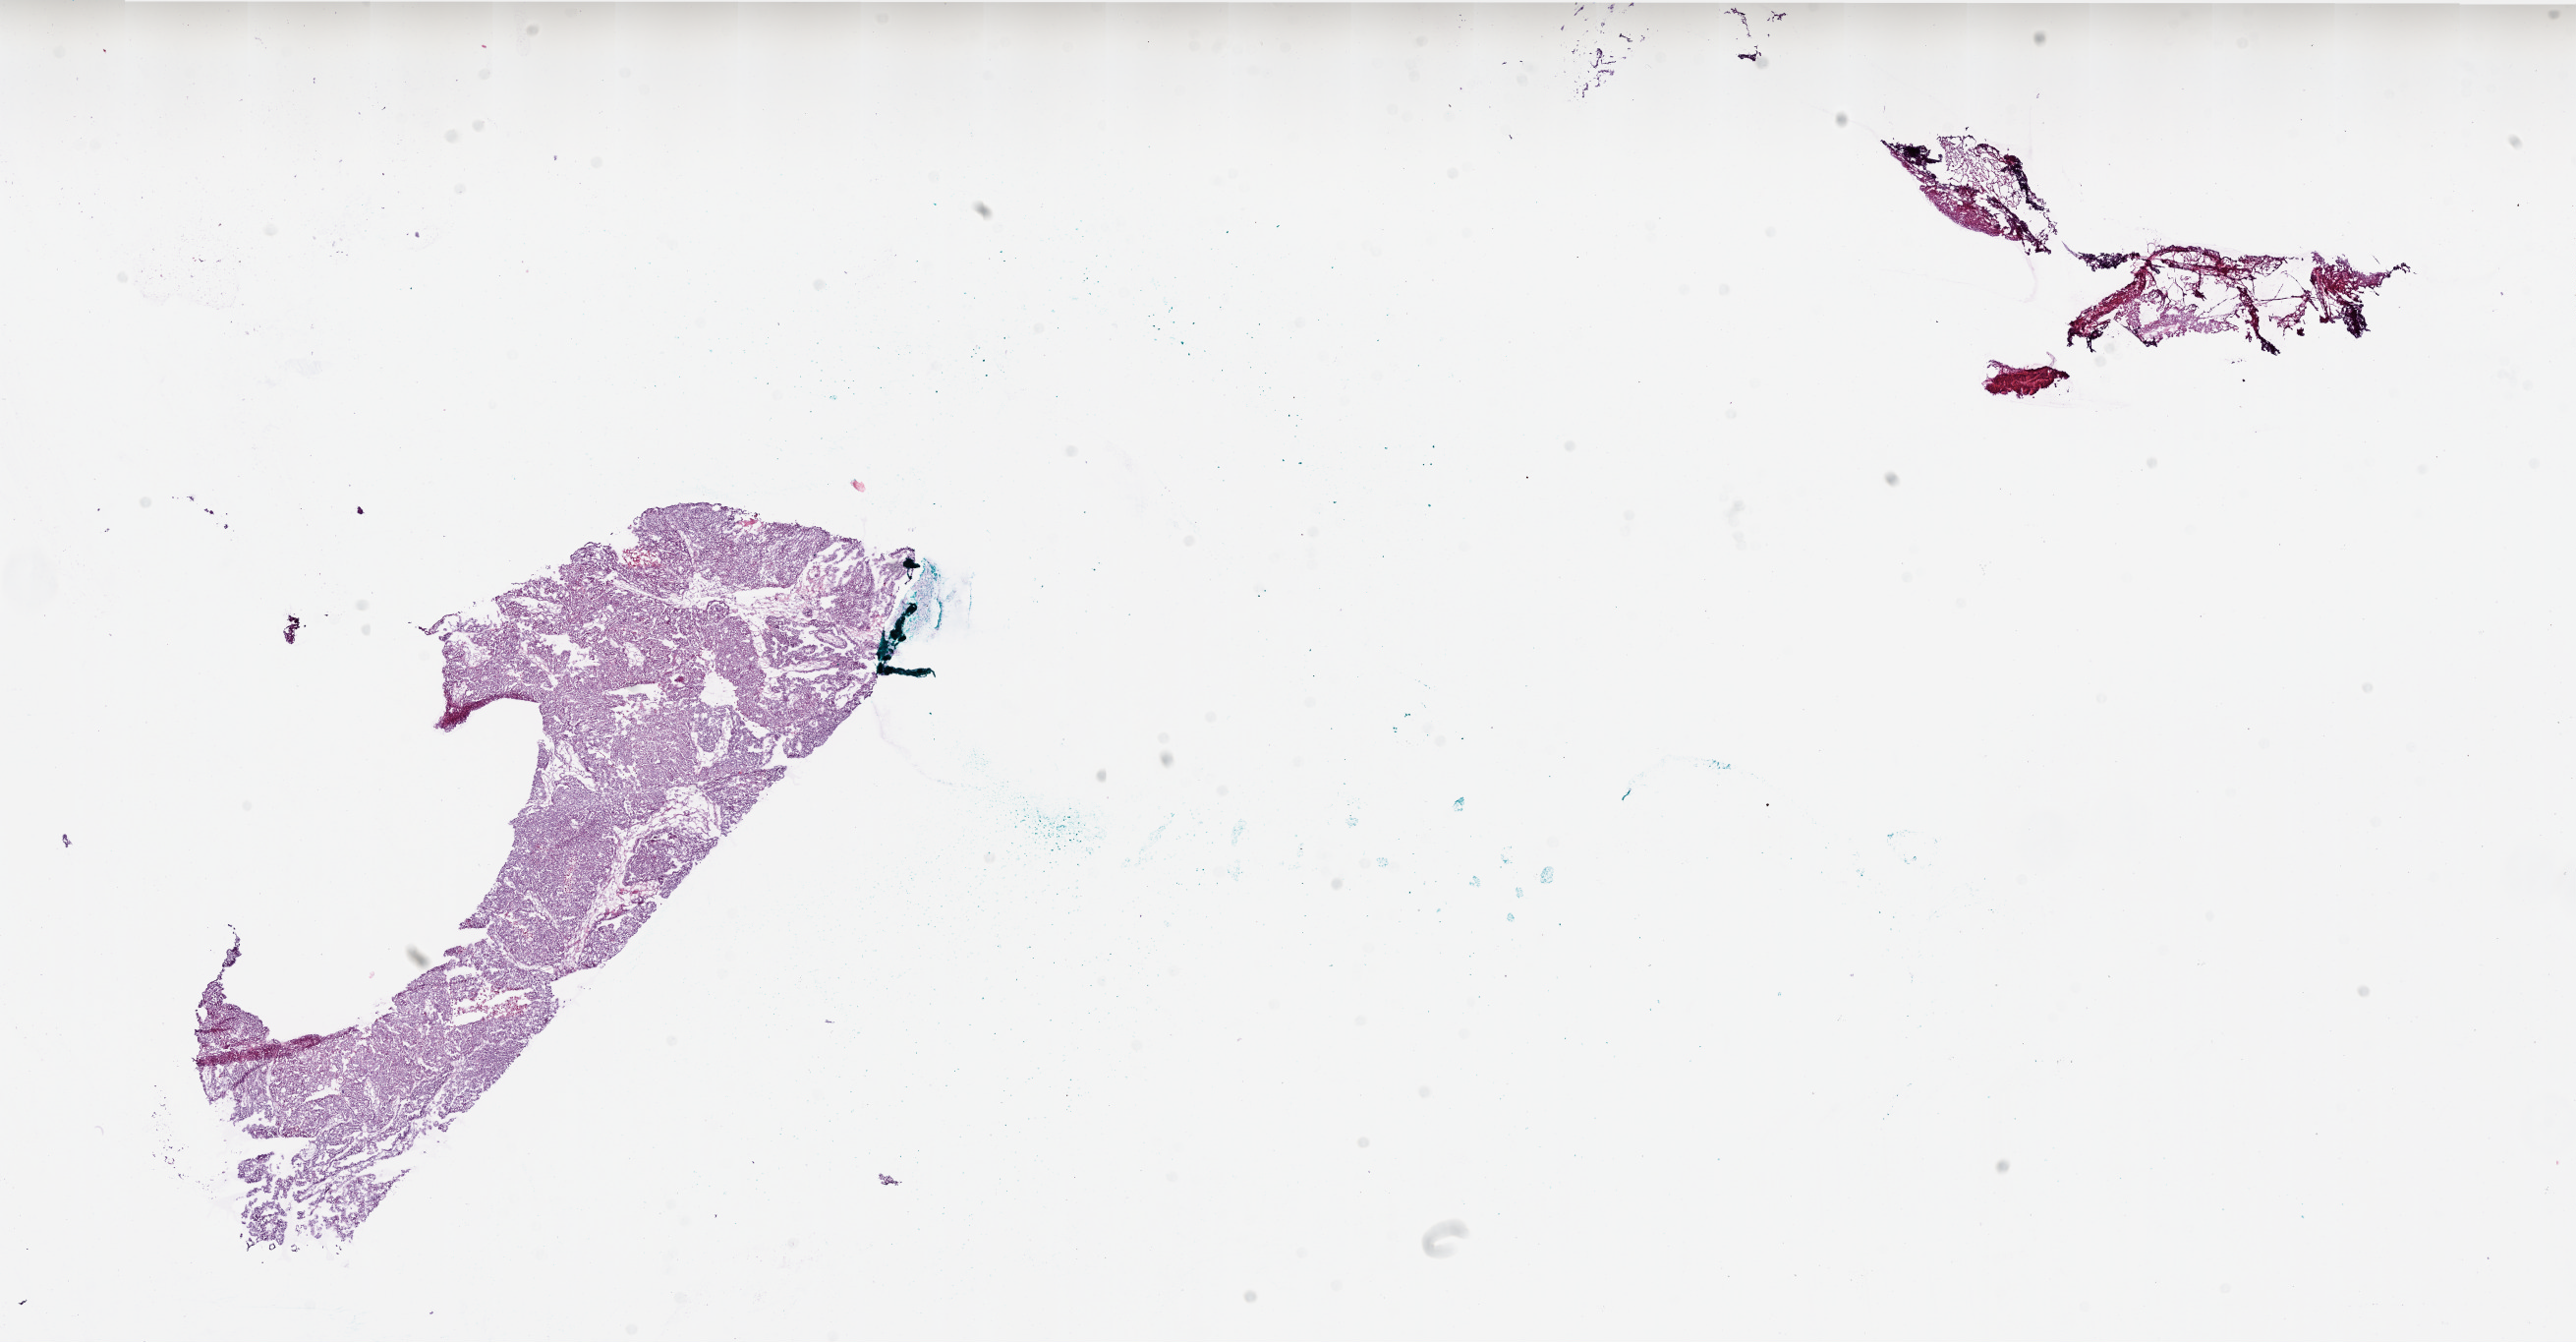
H&E whole-slide image, a low-resolution overview of the entire scanned area, about 21.0 x 10.9 mm (slide scanned at 20x). Frozen section from the bottom of the tissue portion. Sample: primary tumour, ovary. Patient: female, age at initial diagnosis 67 years. Histologic grade: G3 (poorly differentiated). Slide review estimates, as recorded: tumour cells 95%, tumour nuclei 98%, normal cells 0%, stromal cells 5%, necrosis 0%.
* laterality: bilateral
* diagnosis: Serous cystadenocarcinoma, NOS
* FIGO stage: IIIC